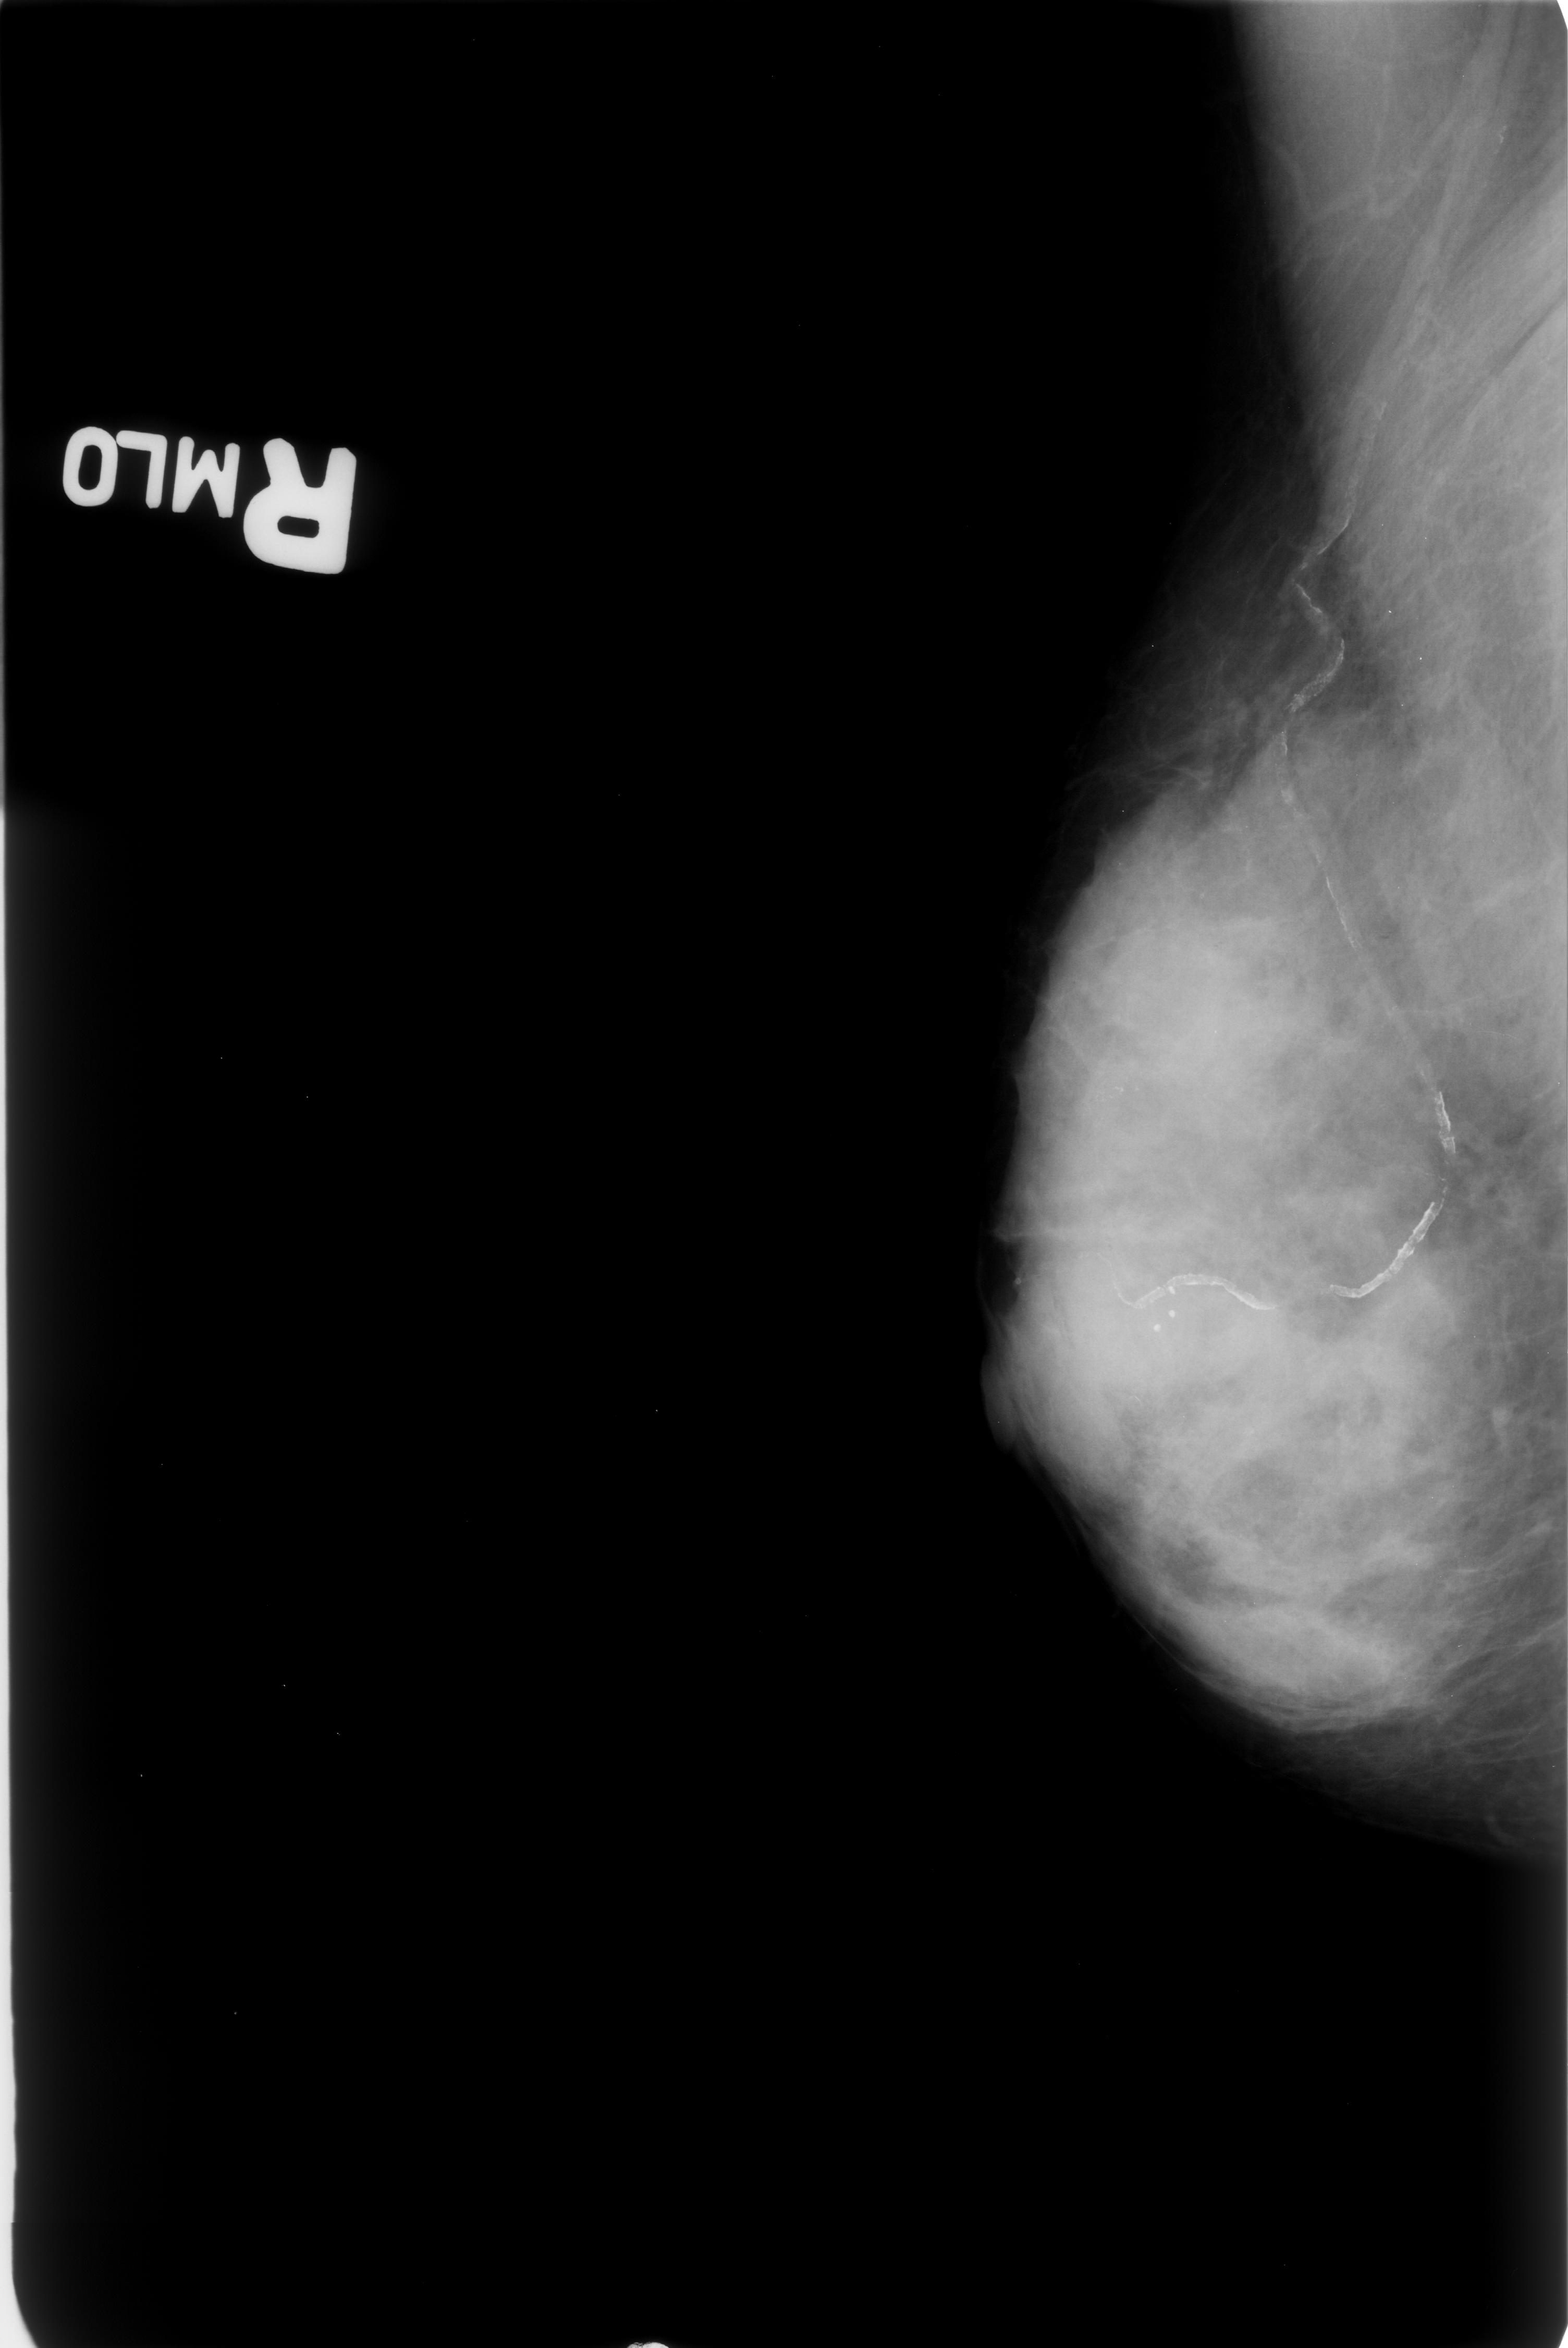
Mammogram (digitized film); right breast; MLO view; breast composition: extremely dense (BI-RADS density category 4 of 4); 1568 × 2348 image matrix.
Marked abnormalities (boxes around the expert regions of interest):
- calcifications, morphology pleomorphic, distribution clustered; BI-RADS assessment category 4; pathology (as recorded): benign: box from (x=1088, y=1055) to (x=1152, y=1131) px